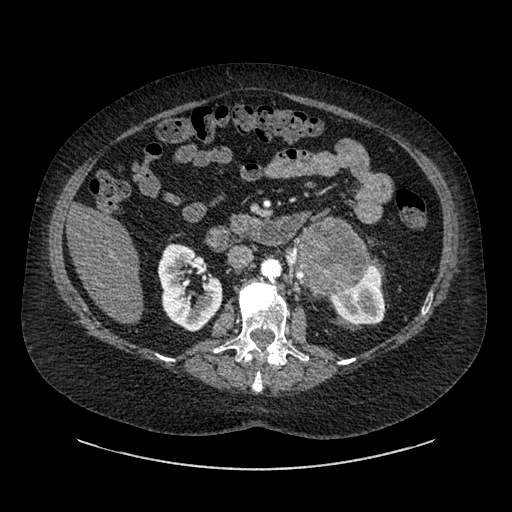
Contrast-enhanced abdominal CT, one axial slice; slice 513 of 769 in the series (ordered by position); reconstruction kernel SOFT; soft-tissue window (W 400 / L 40 HU); 0.62 mm slice thickness; 512 × 512 image matrix. Female patient, age 61 years. From the clinical record (not read from this slice): diagnosis: adrenocortical carcinoma; tumour side: left adrenal; tumour size at pathology: 13 cm; Ki-67 index: 79 %; stage (as recorded): 2.
Outlined on this slice (semi-automatic segmentation, software-assisted and operator-edited):
- mass: bounding box <300,222,367,288> (left, top, right, bottom; pixels)